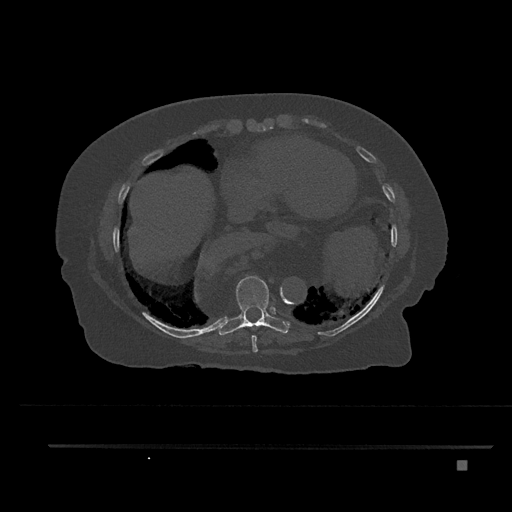
CT including the spine, one axial slice. Position 408 of 797 along the scan axis. Reconstruction kernel Br40s/3. 120 kVp. Bone window (W 1800 / L 400 HU). 0.5 mm slice thickness. 512 × 512 image matrix. Patient: female, 76 years. Case-level facts recorded for this patient, not image findings: primary cancer: lung; vertebrae with lytic lesions (as recorded): T11, L3.
Structures marked on this image (semi-automatic segmentation, software-assisted and operator-edited):
- T8 vertebra: bounding box <251,335,258,352> (left, top, right, bottom; pixels)
- T9 vertebra: <217,275,289,336>